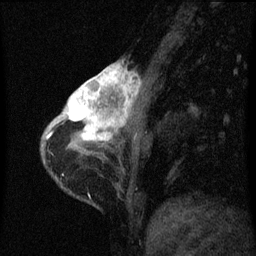
Breast MRI (dynamic contrast-enhanced), one sagittal slice; position 15 of 60 along the scan axis; dynamic contrast-enhanced series, image 2 of 3 at this slice position (ordered by acquisition); 1.5 T; TE 4.2 ms, TR 8 ms; 2 mm slice thickness; 256 × 256 image matrix. Female patient, age 38 years.
Annotated regions visible in this slice (semi-automatic segmentation, software-assisted and operator-edited):
- analysis volume of interest (the breast-tissue region the enhancement analysis was run in; not a lesion): bounding box (x1, y1, x2, y2) in pixels: (61, 66, 139, 147)
- tumour enhancement mask (voxels above the 70 % enhancement threshold inside the analysis volume of interest): (64, 66, 139, 143)